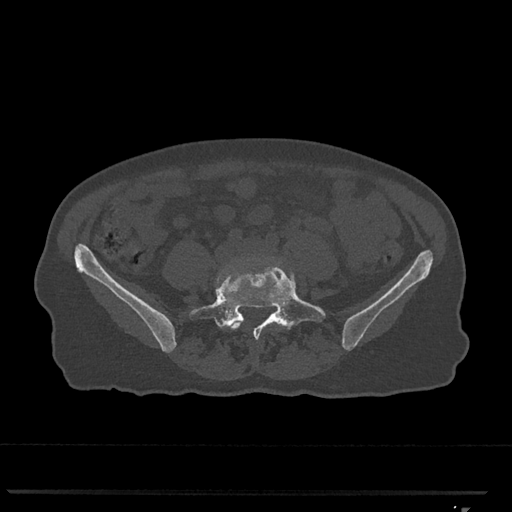
CT including the spine, one axial slice; slice 166 of 793 in the series (ordered by position); reconstruction kernel Br40s/3; bone window (W 1800 / L 400 HU); 0.5 mm slice thickness; 512 × 512 image matrix. Female patient, age 62 years. Case-level facts recorded for this patient, not image findings: primary cancer: renal.
Outlined on this slice (semi-automatically segmented with operator editing):
- L4 vertebra: box from (x=217, y=258) to (x=281, y=330) px
- L5 vertebra: (x=189, y=262)–(x=326, y=339)